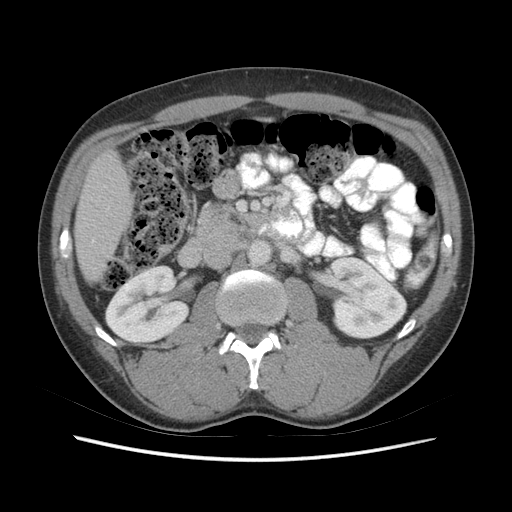
Contrast-enhanced abdominal CT (liver protocol), one axial slice; slice 16 of 73 in the series (ordered by position); 140 kVp; soft-tissue window (W 400 / L 40 HU); 2.5 mm slice thickness; 512 × 512 image matrix, field of view 360 × 360 mm. Case-level facts recorded for this patient, not image findings: diagnosis: hepatocellular carcinoma (patient treated with transarterial chemoembolisation; whether this scan precedes or follows treatment is not stated here); TNM stage (as recorded): Stage-IIIA; Child-Pugh class: A; tumour nodularity: multinodular; tumour size: 6.6 cm.
Annotated regions visible in this slice (semi-automatic segmentation, software-assisted and operator-edited):
- liver parenchyma outside the tumour (the mass and vessels are separate outlines, so this box may not span the whole liver): bounding box (x1, y1, x2, y2) in pixels: (74, 150, 132, 280)